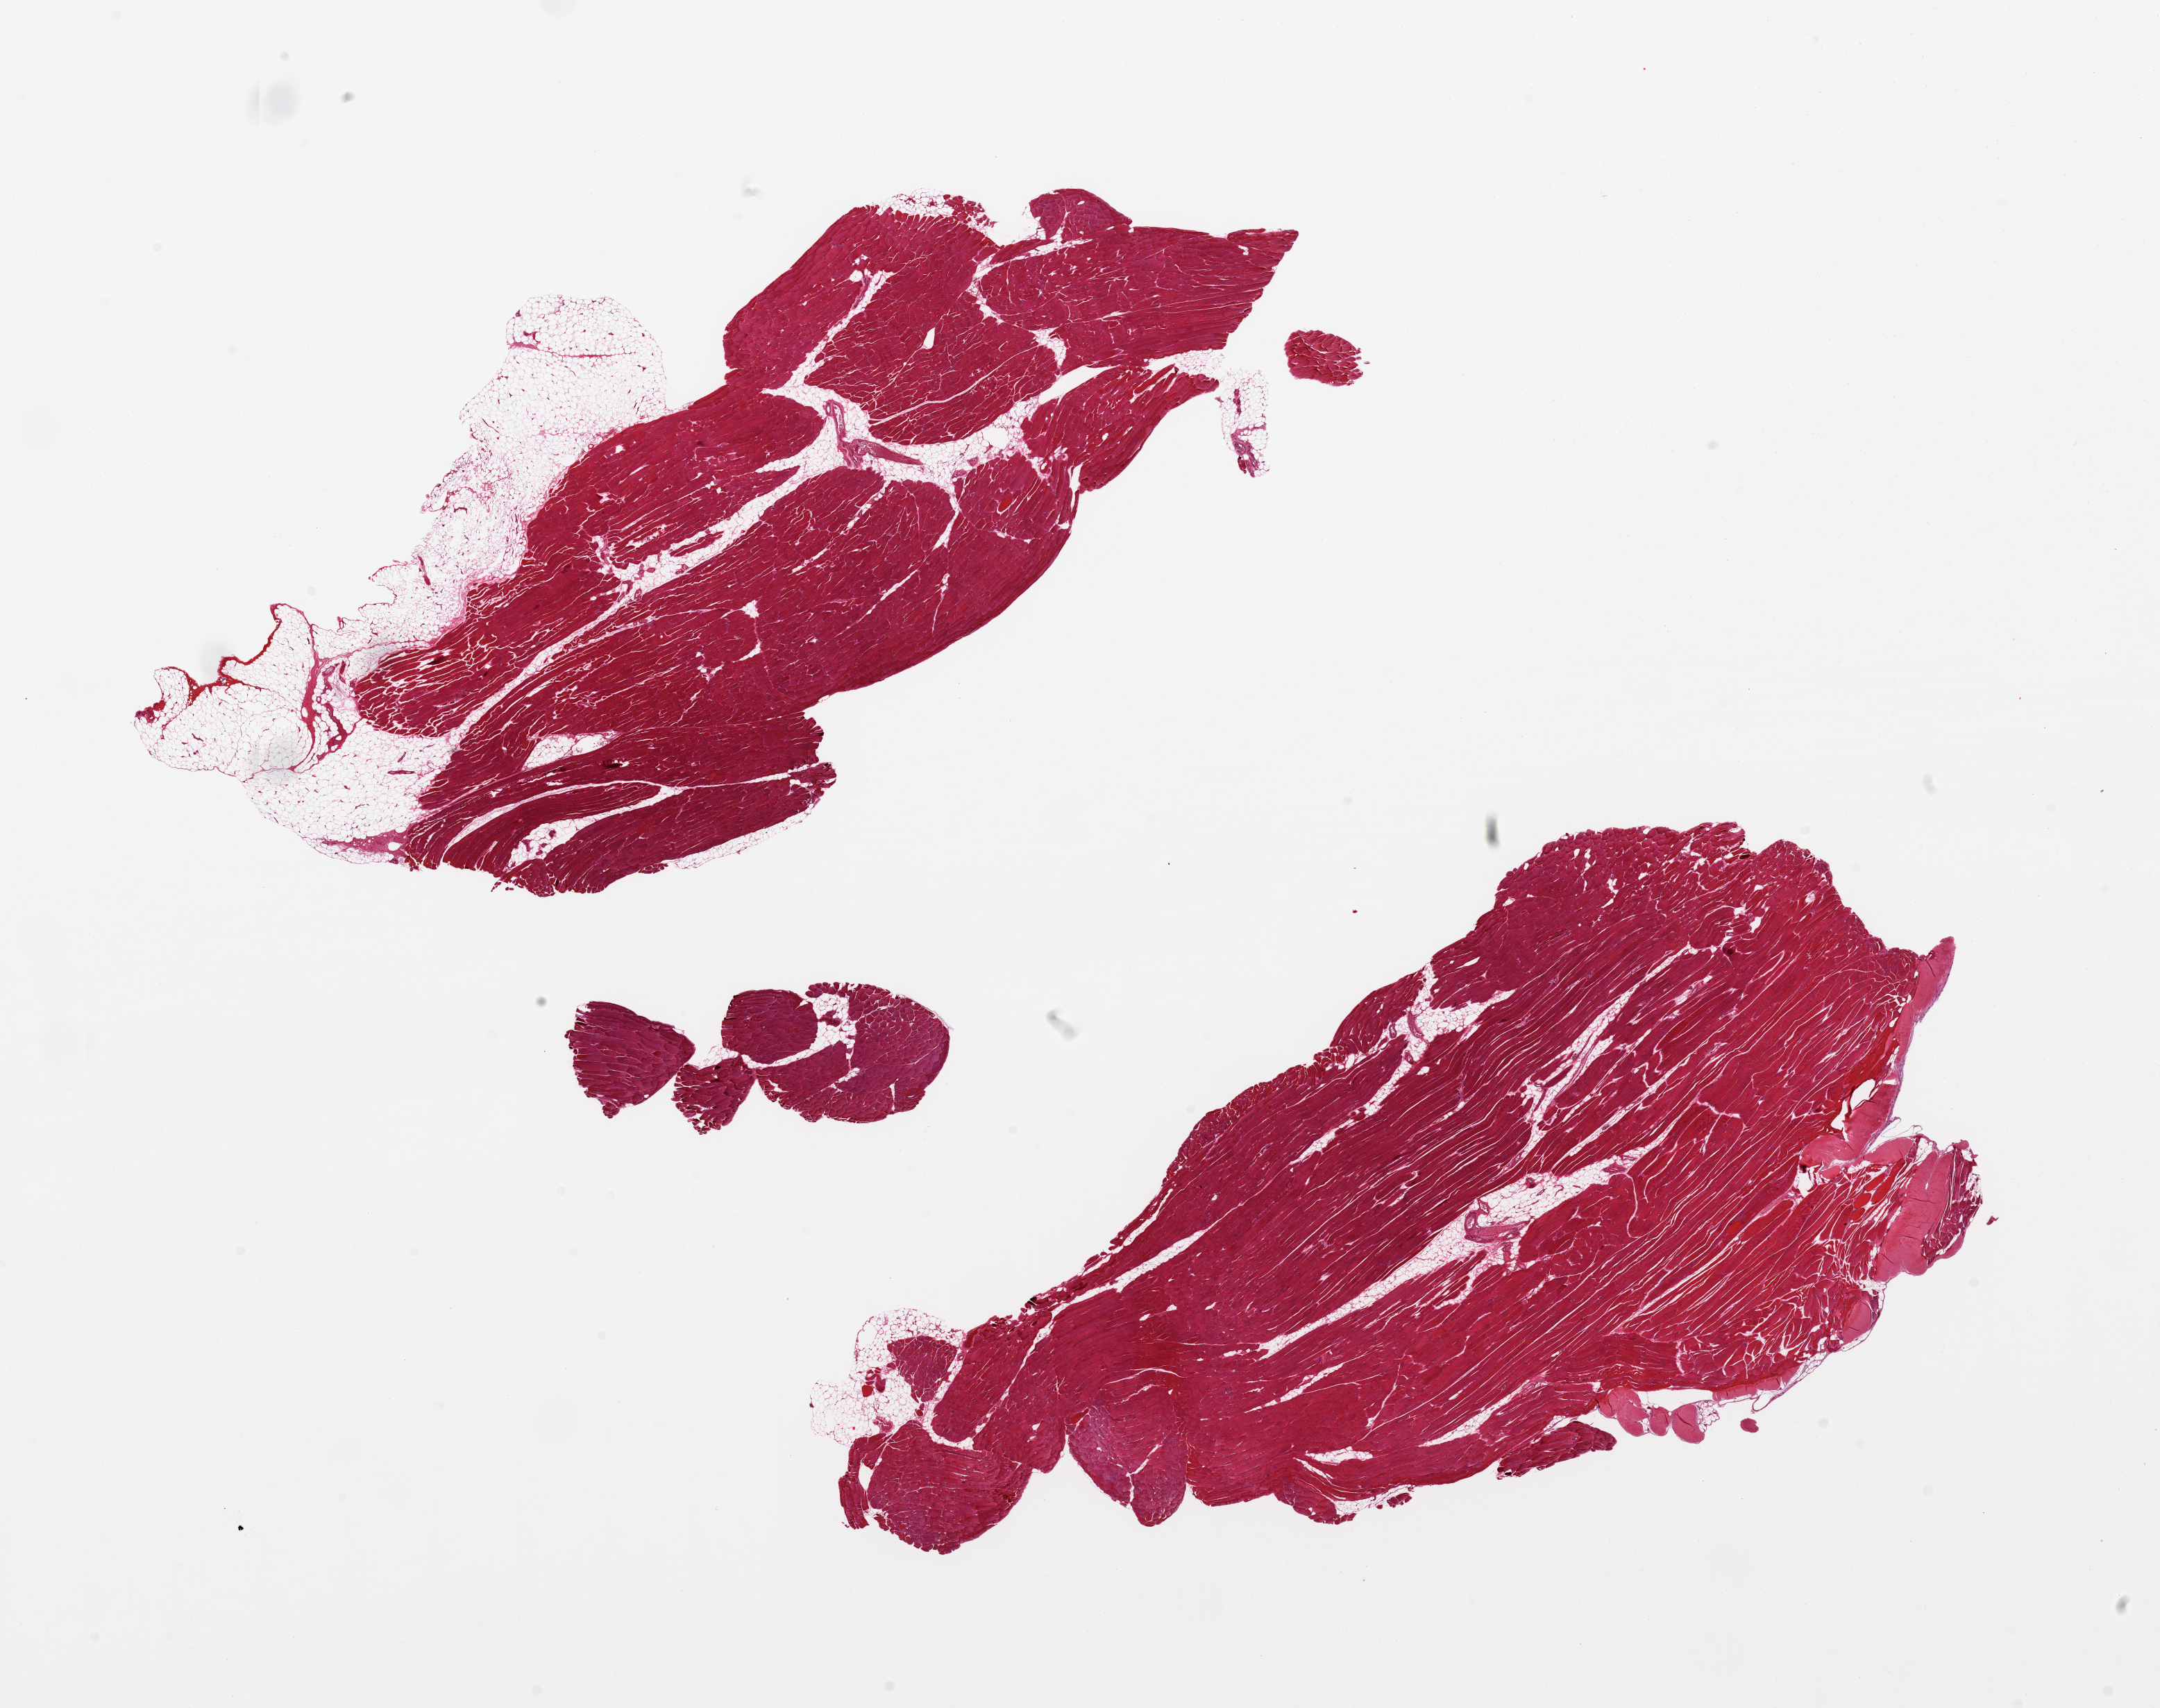
Whole-slide image, haematoxylin and eosin stain, brightfield, a low-resolution overview of the entire scanned area, about 24.6 x 19.5 mm (acquisition: 20x scan), PAXgene-fixed, paraffin-embedded tissue, target tissue: skeletal muscle, tissue donor sample. Donor: female.
• reviewer comment on this tissue sample: 2 pieces ~10% adherent/interstitial fat